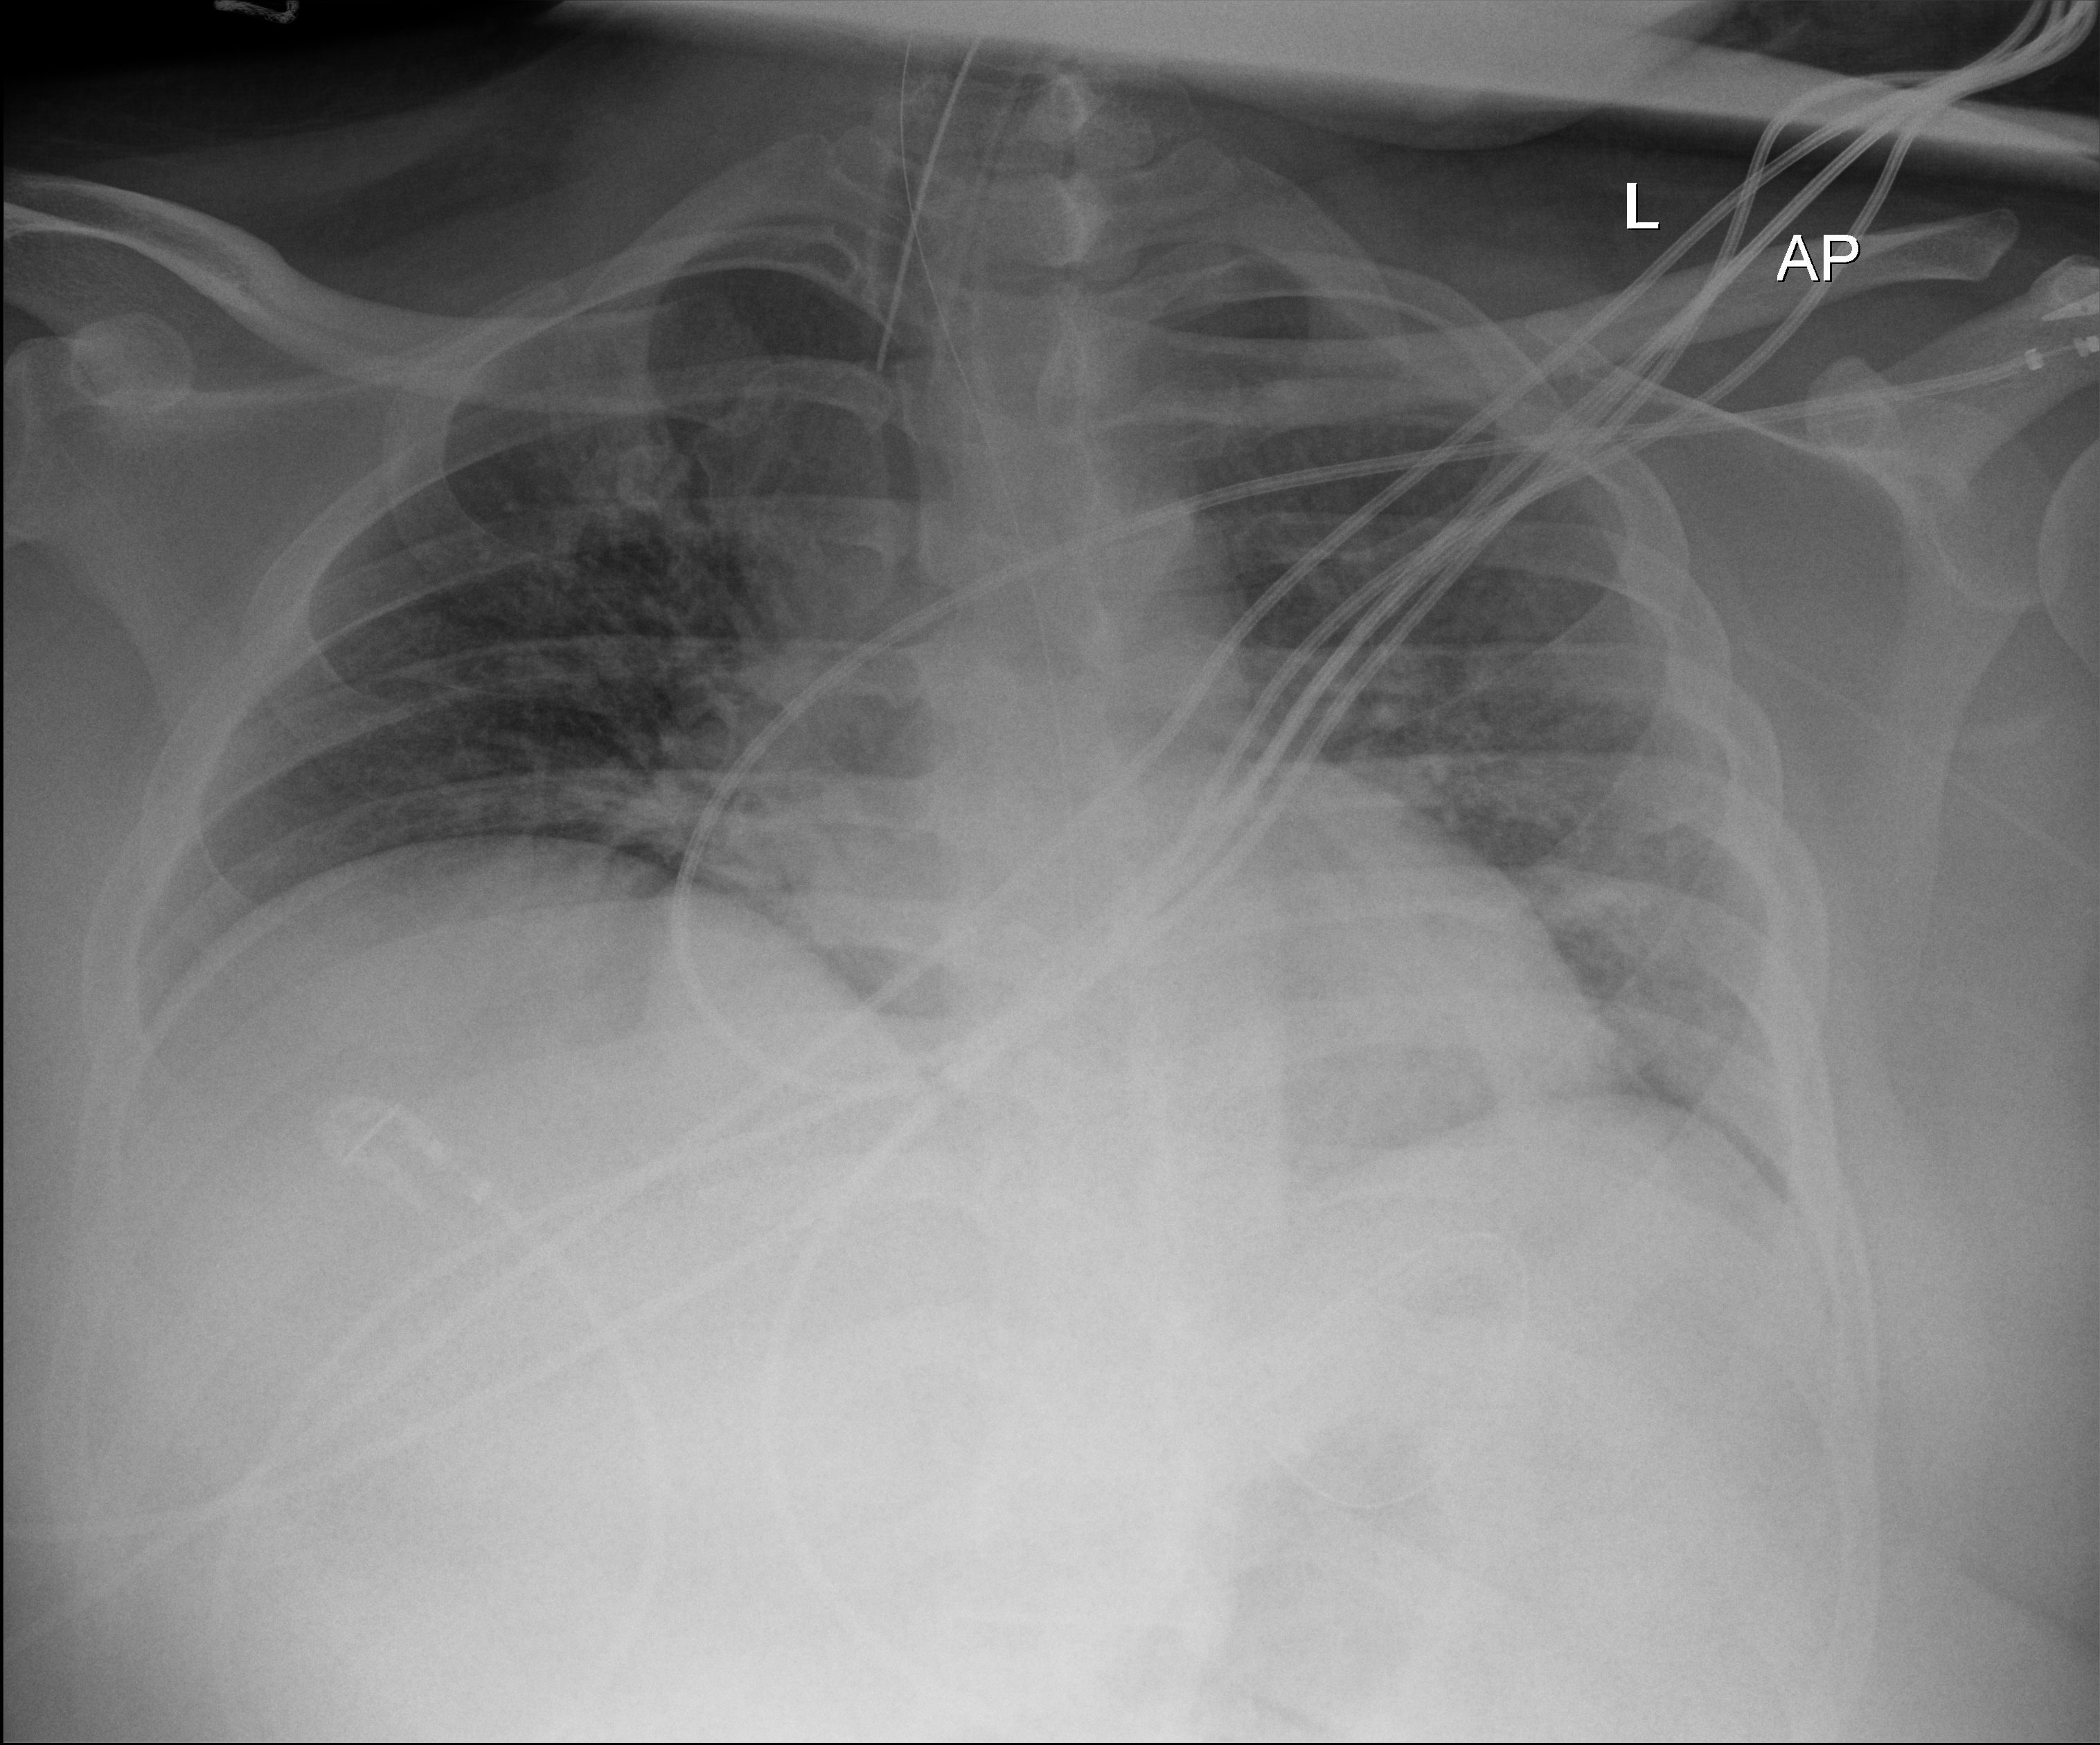
Chest X-ray (portable). Patient hospitalised with COVID-19; male, aged 18–59 years.
Hospital-stay facts (about this admission, not read from this image; timing relative to this image not recorded): admitted to intensive care during this hospital stay: yes.